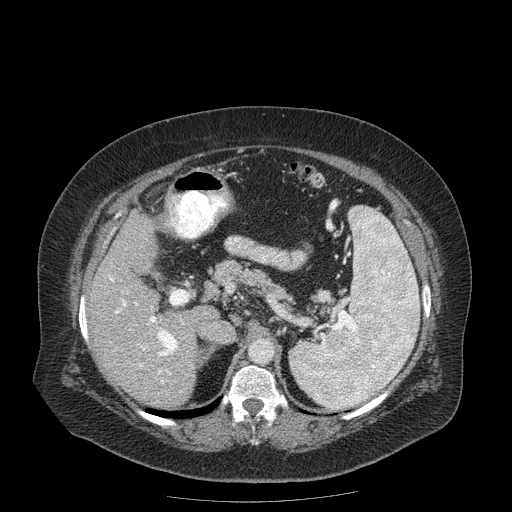
Contrast-enhanced abdominal CT (liver protocol), one axial slice; position 103 of 204 along the scan axis; 120 kVp; soft-tissue window (W 400 / L 40 HU); 2.5 mm slice thickness; 512 × 512 image matrix. Case-level facts recorded for this patient, not image findings: diagnosis: hepatocellular carcinoma (patient treated with transarterial chemoembolisation; whether this scan precedes or follows treatment is not stated here); TNM stage (as recorded): Stage-IIIB; Child-Pugh class: A; tumour differentiation: well differentiated.
Structures marked on this image (semi-automatic segmentation, software-assisted and operator-edited):
- liver parenchyma outside the tumour (the mass and vessels are separate outlines, so this box may not span the whole liver): bounding box (x1, y1, x2, y2) in pixels: (88, 210, 202, 408)
- liver vessels: (109, 276, 178, 382)